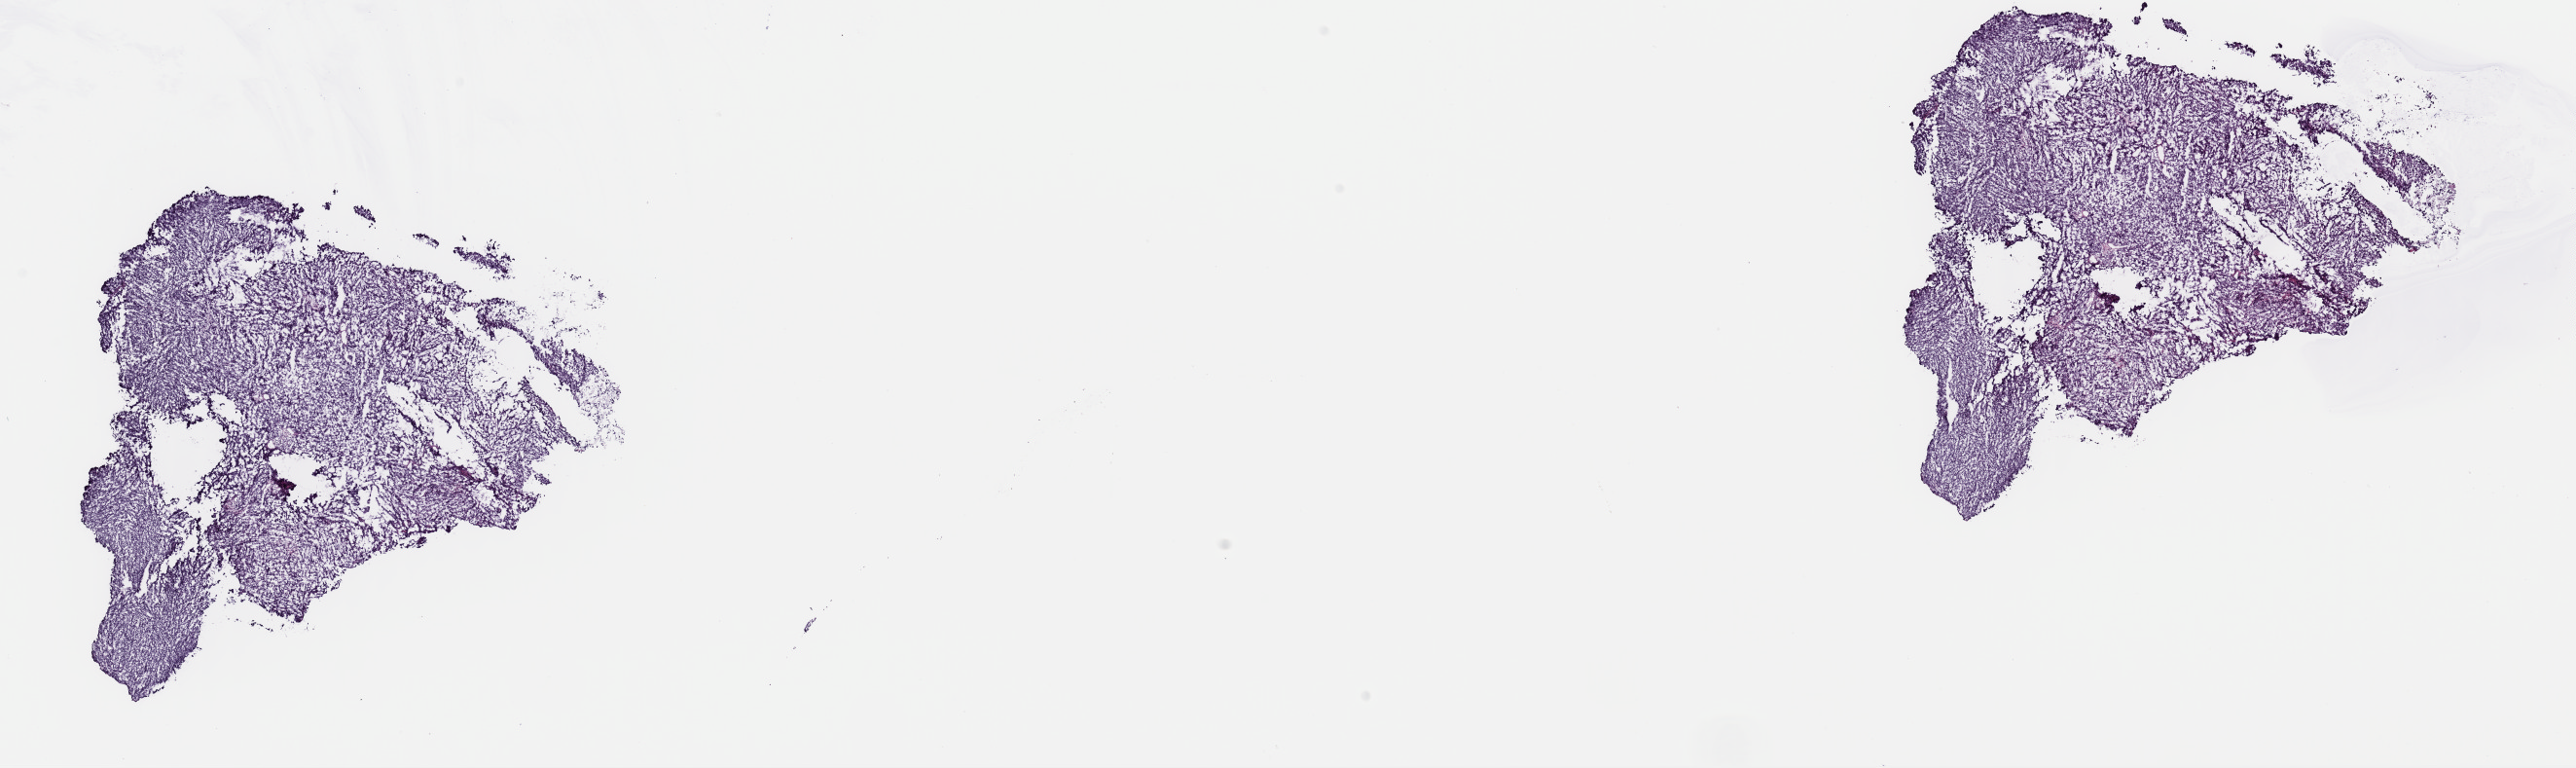
Digitized H&E tissue section (whole slide), low-resolution overview of the scanned area, about 20.9 x 6.2 mm. Frozen section from the top of the tissue portion. Metastatic tumour sample, sampled site: connective, subcutaneous and other soft tissues of thorax. Patient: male, age at initial diagnosis 59 years. Pathologist review of this section (percent, as recorded): tumour cells 90%, tumour nuclei 90%, normal cells 0%, stromal cells 10%, necrosis 0%. Inflammatory infiltration, as recorded: lymphocyte infiltration 0%, monocyte infiltration 0%, neutrophil infiltration 0%.
This section: metastatic tumour tissue. Patient diagnosis: Malignant melanoma, NOS.